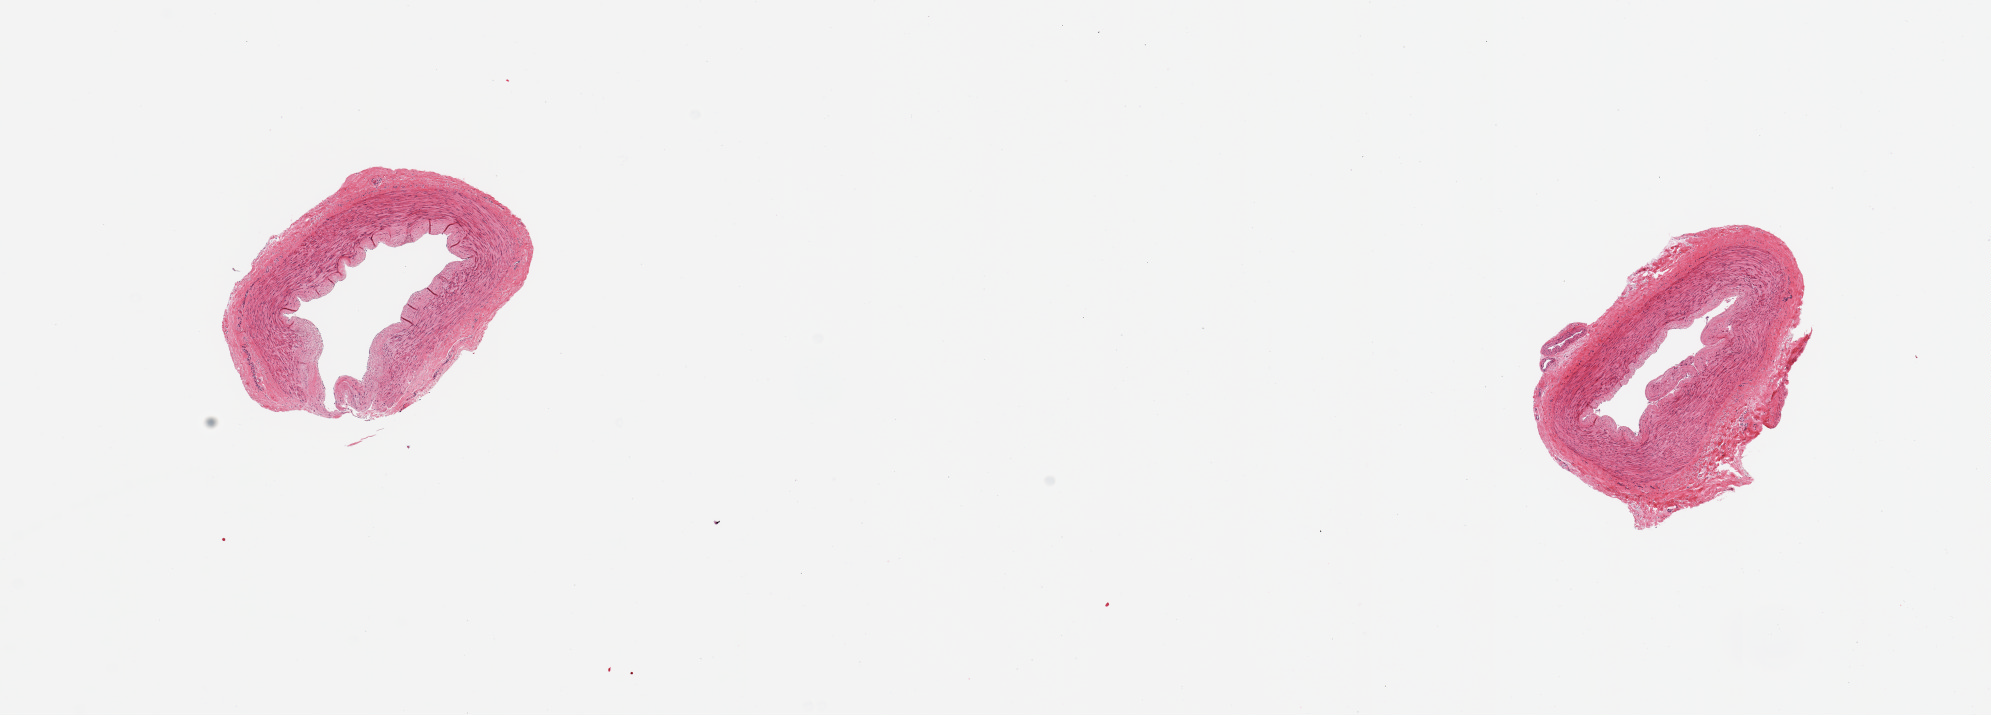
Whole-slide image, H&E stain — low-resolution overview of the scanned area, about 15.8 x 5.7 mm, PAXgene-fixed paraffin-embedded (PFPE) section, target tissue: tibial artery, tissue donor sample.
Reviewer comment on this tissue sample: 2 pieces; well trimmed.